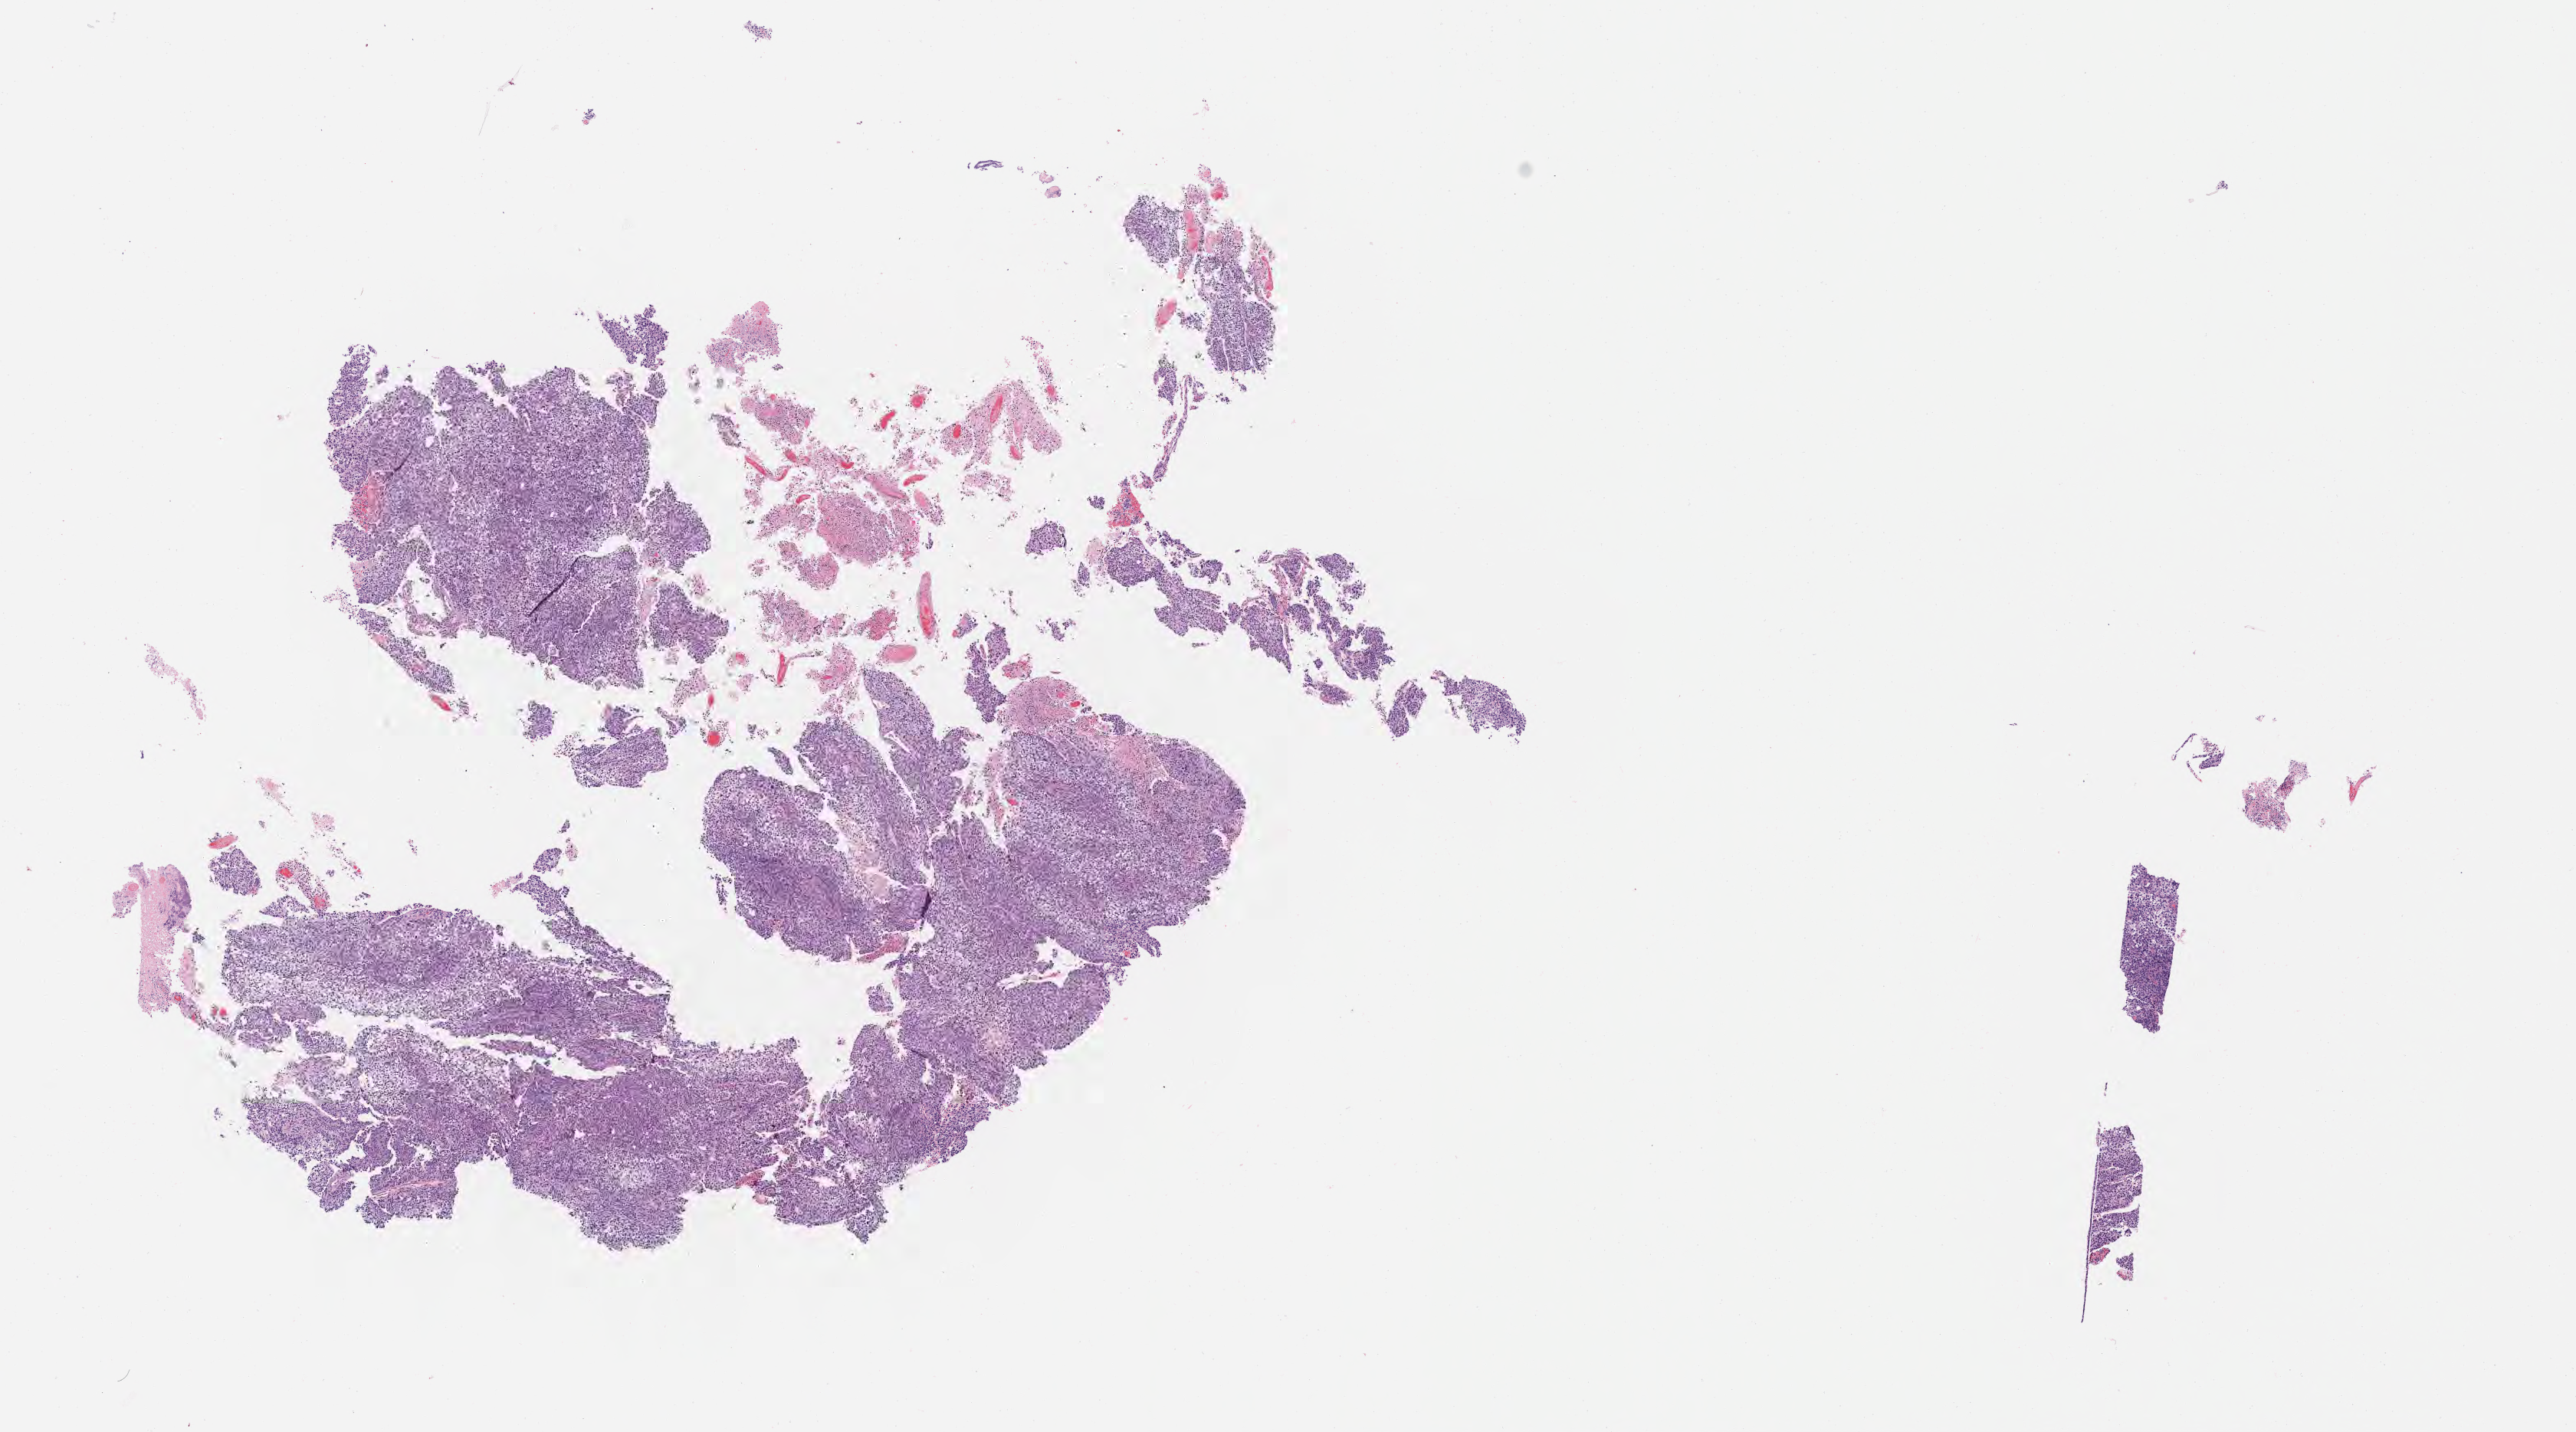
Digitized hematoxylin and eosin (H&E)-stained section — shown as a low-resolution overview of the whole scanned area (about 13.6 x 7.6 mm), specimen: tumor tissue, anatomic site: cervix. Female patient, 30 years old.
• diagnosis: Squamous cell carcinoma, large cell, nonkeratinizing, NOS